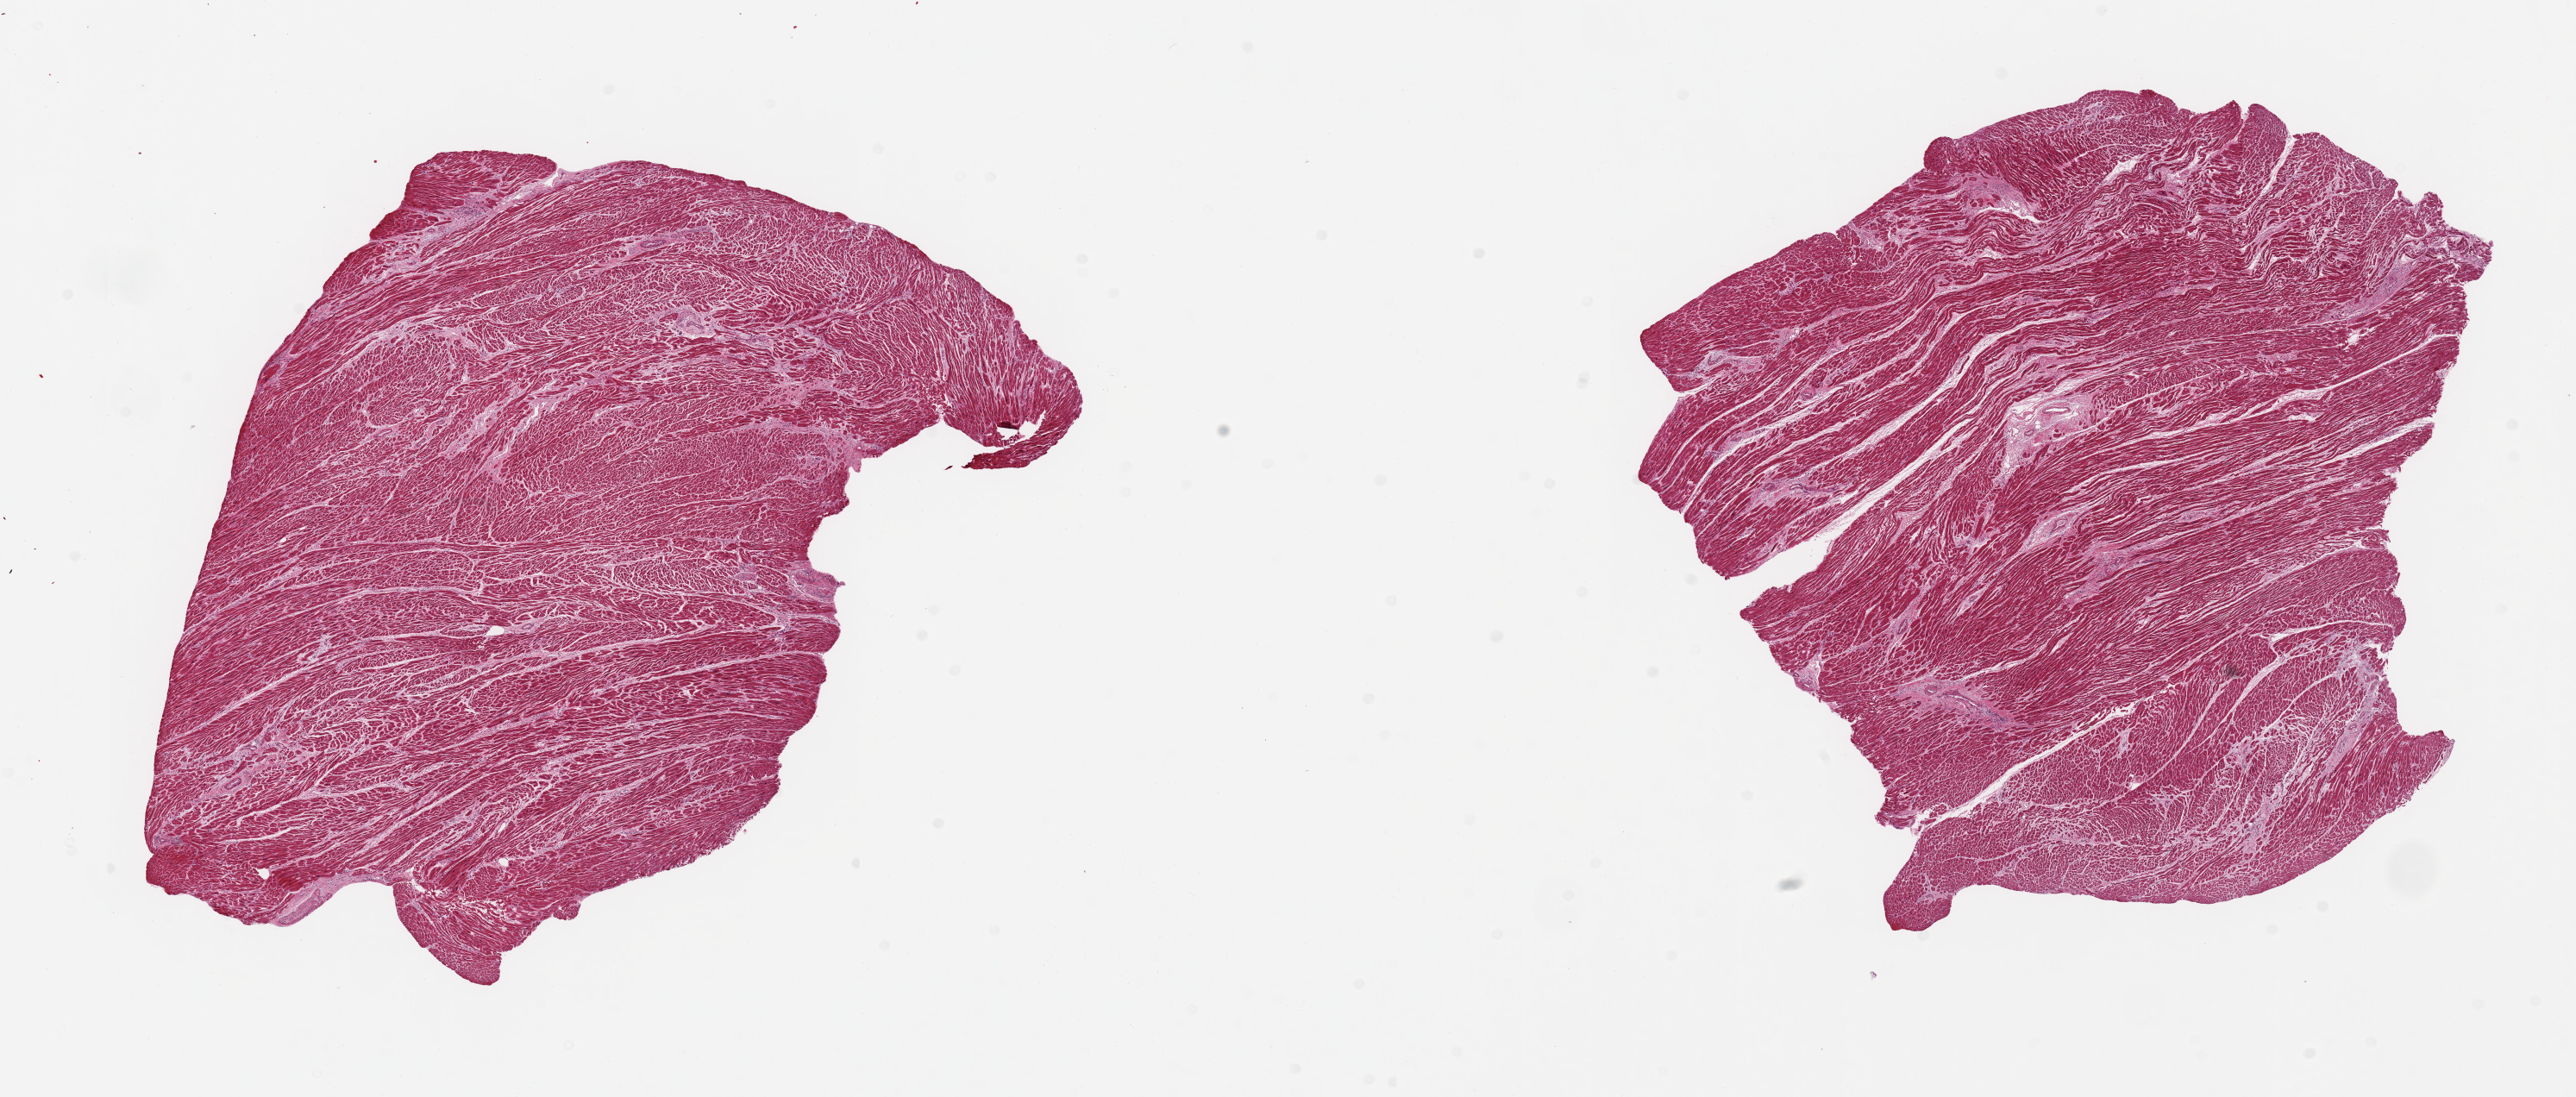
Whole-slide image, H&E stain, low-resolution overview of the scanned area, about 23.6 x 10.1 mm (acquisition: 20x scan). PAXgene-fixed paraffin-embedded (PFPE) section. Section of heart (target tissue). Tissue donor sample. Donor sex: female.
Pathologist's review note for this sample: 2 pieces, marked interstitial fibrosis/chronic ischemic changes.